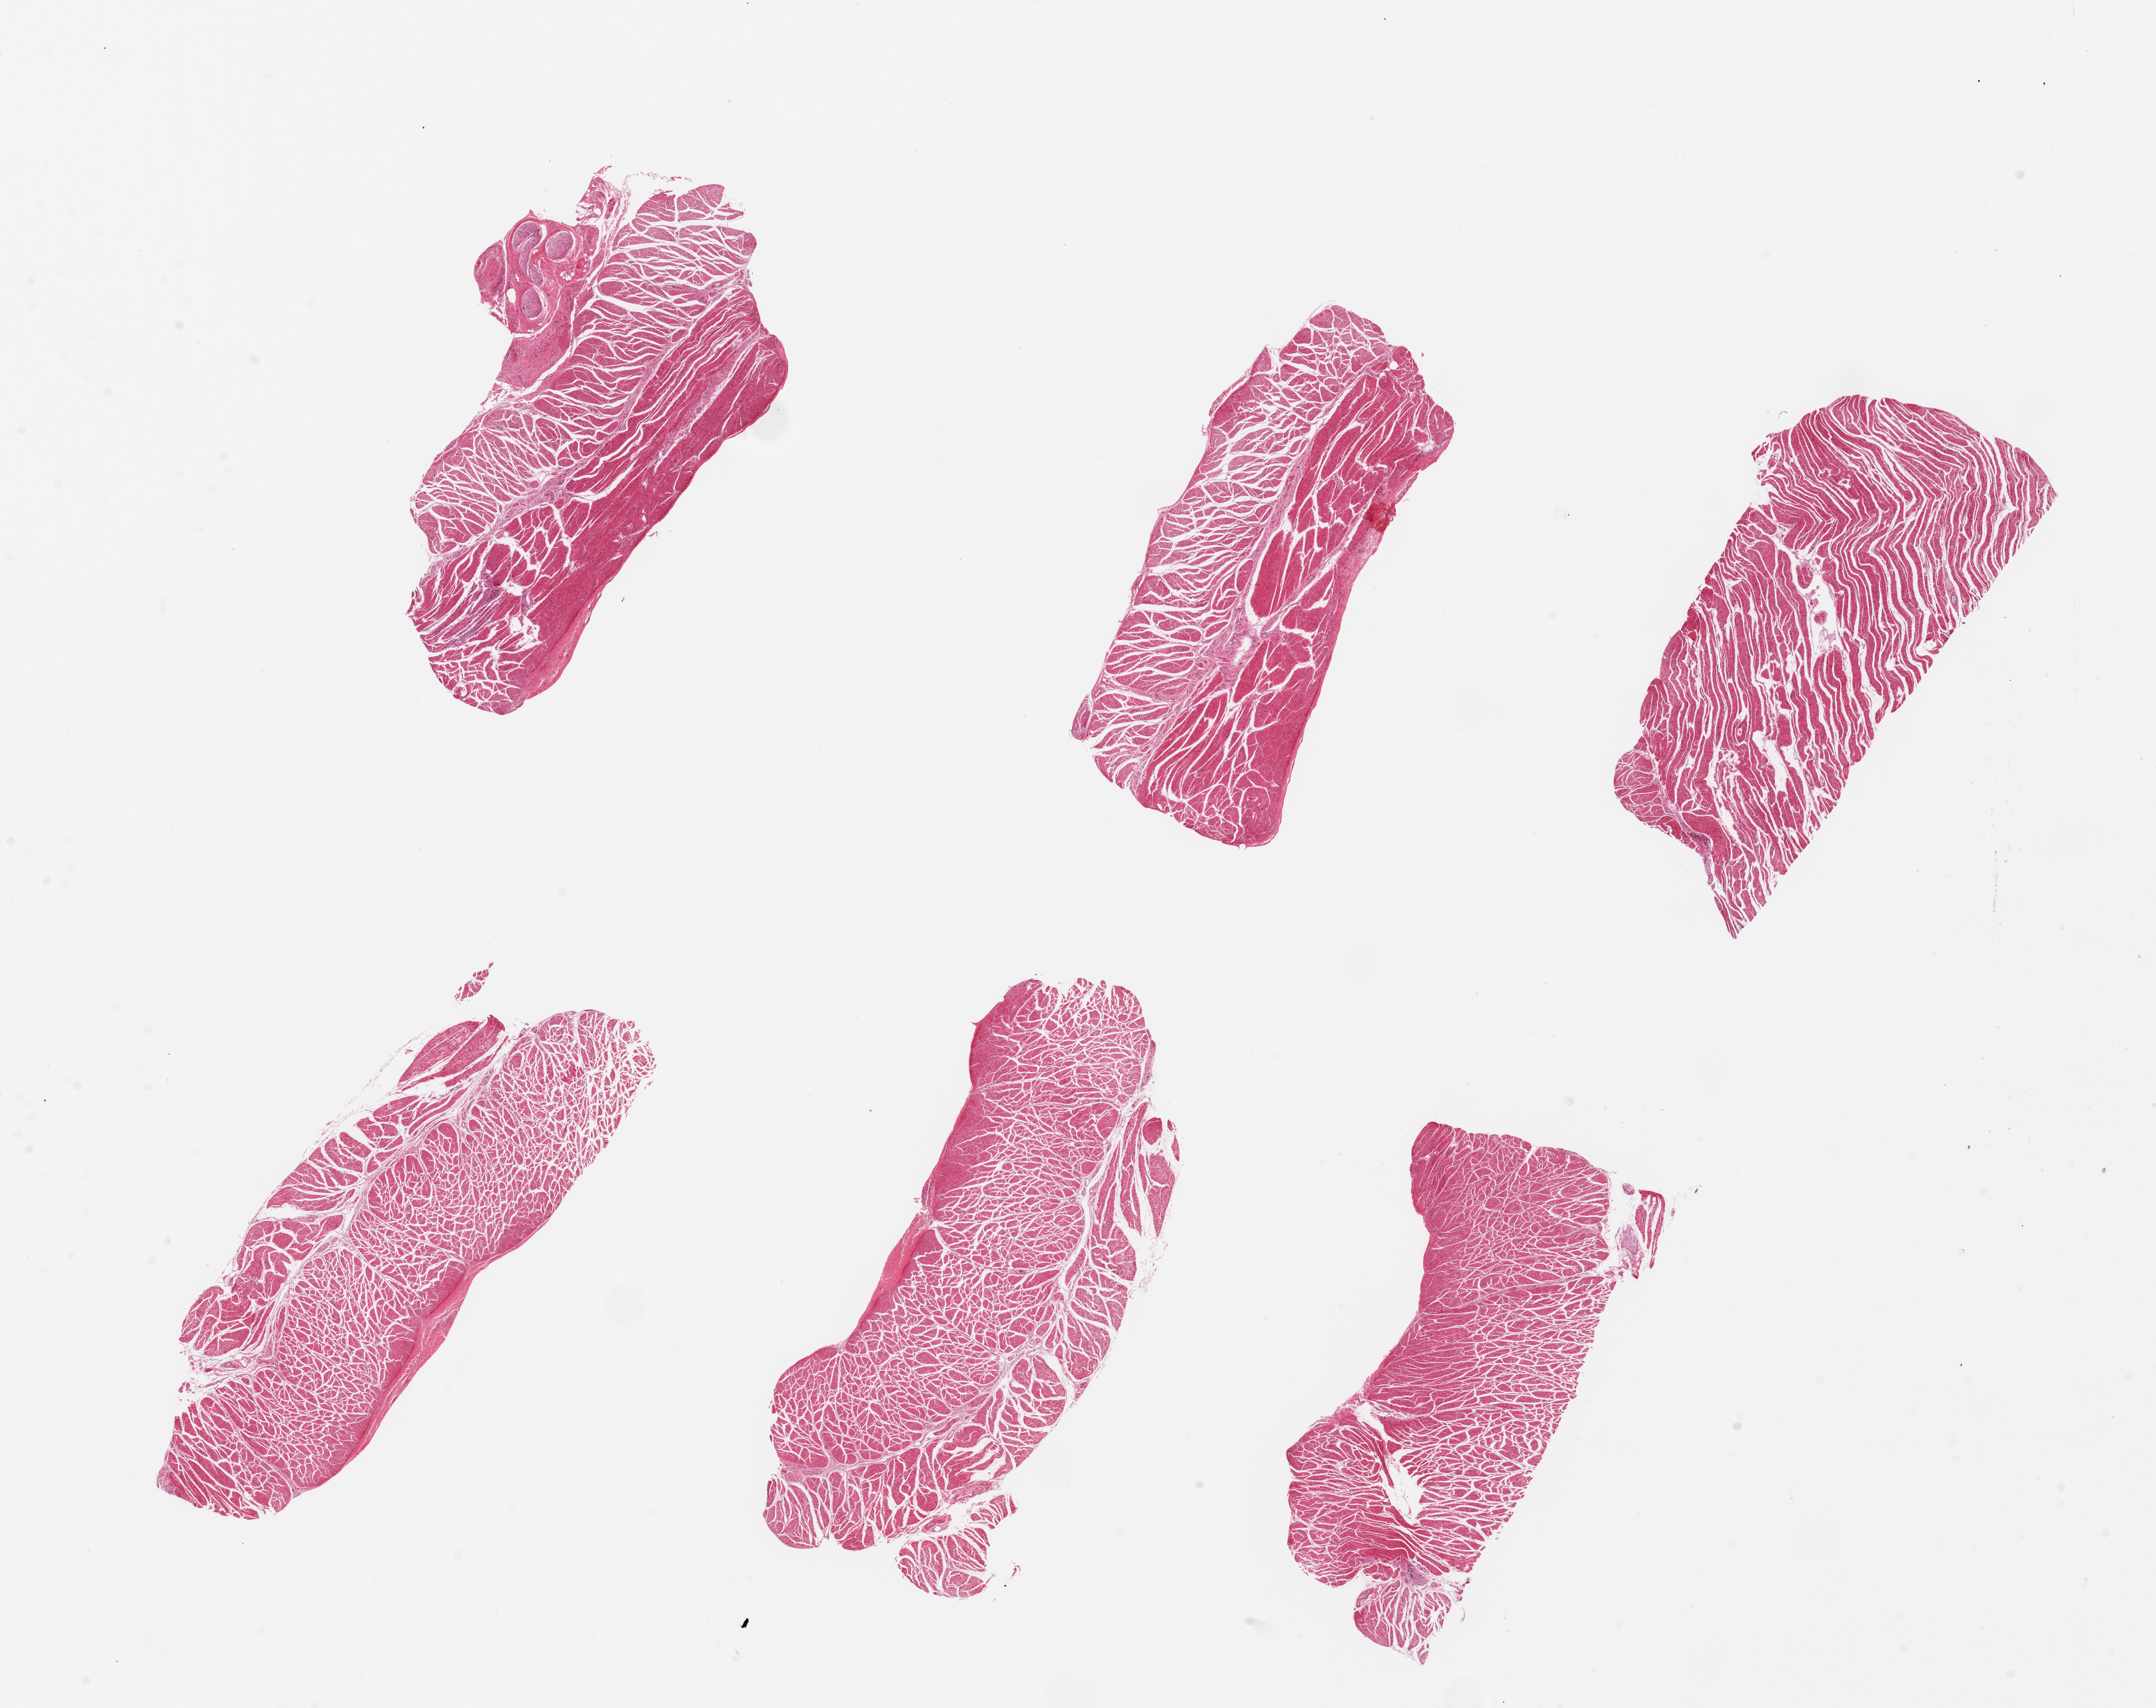
Digitized haematoxylin and eosin-stained section — whole scanned area (about 25.6 x 20.3 mm, acquisition: 20x scan) shown as a low-resolution overview; PAXgene-fixed, paraffin-embedded tissue; target tissue: esophageal muscle; tissue donor sample. Female donor.
Reviewer comment on this tissue sample: 6 pieces. up to 8x3.5mm; well trimmed muscle.